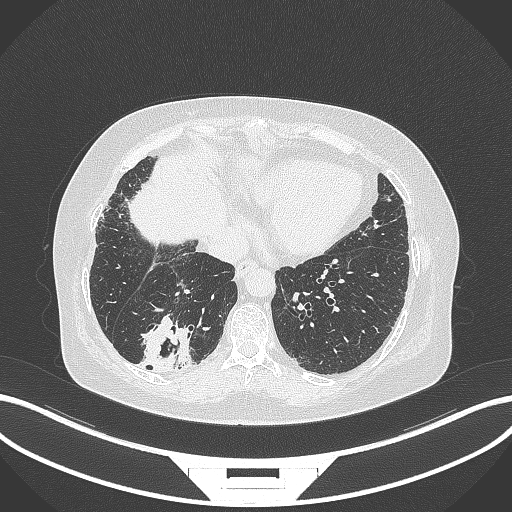
Chest CT, one axial slice. Slice 58 of 296 in the series (ordered by position). 120 kVp. Lung window (W 1500 / L -600 HU). 512 × 512 image matrix, field of view 400 × 400 mm. Female patient, age 65 years. From the clinical record (not read from this slice): clinical TNM (as recorded): T2b N1 M0; histopathological grade: G1.
Outlined on this slice (bounding box drawn by a radiologist):
- lung tumour (recorded histology: adenocarcinoma): bounding box [x1, y1, x2, y2] px = [135, 313, 198, 373]